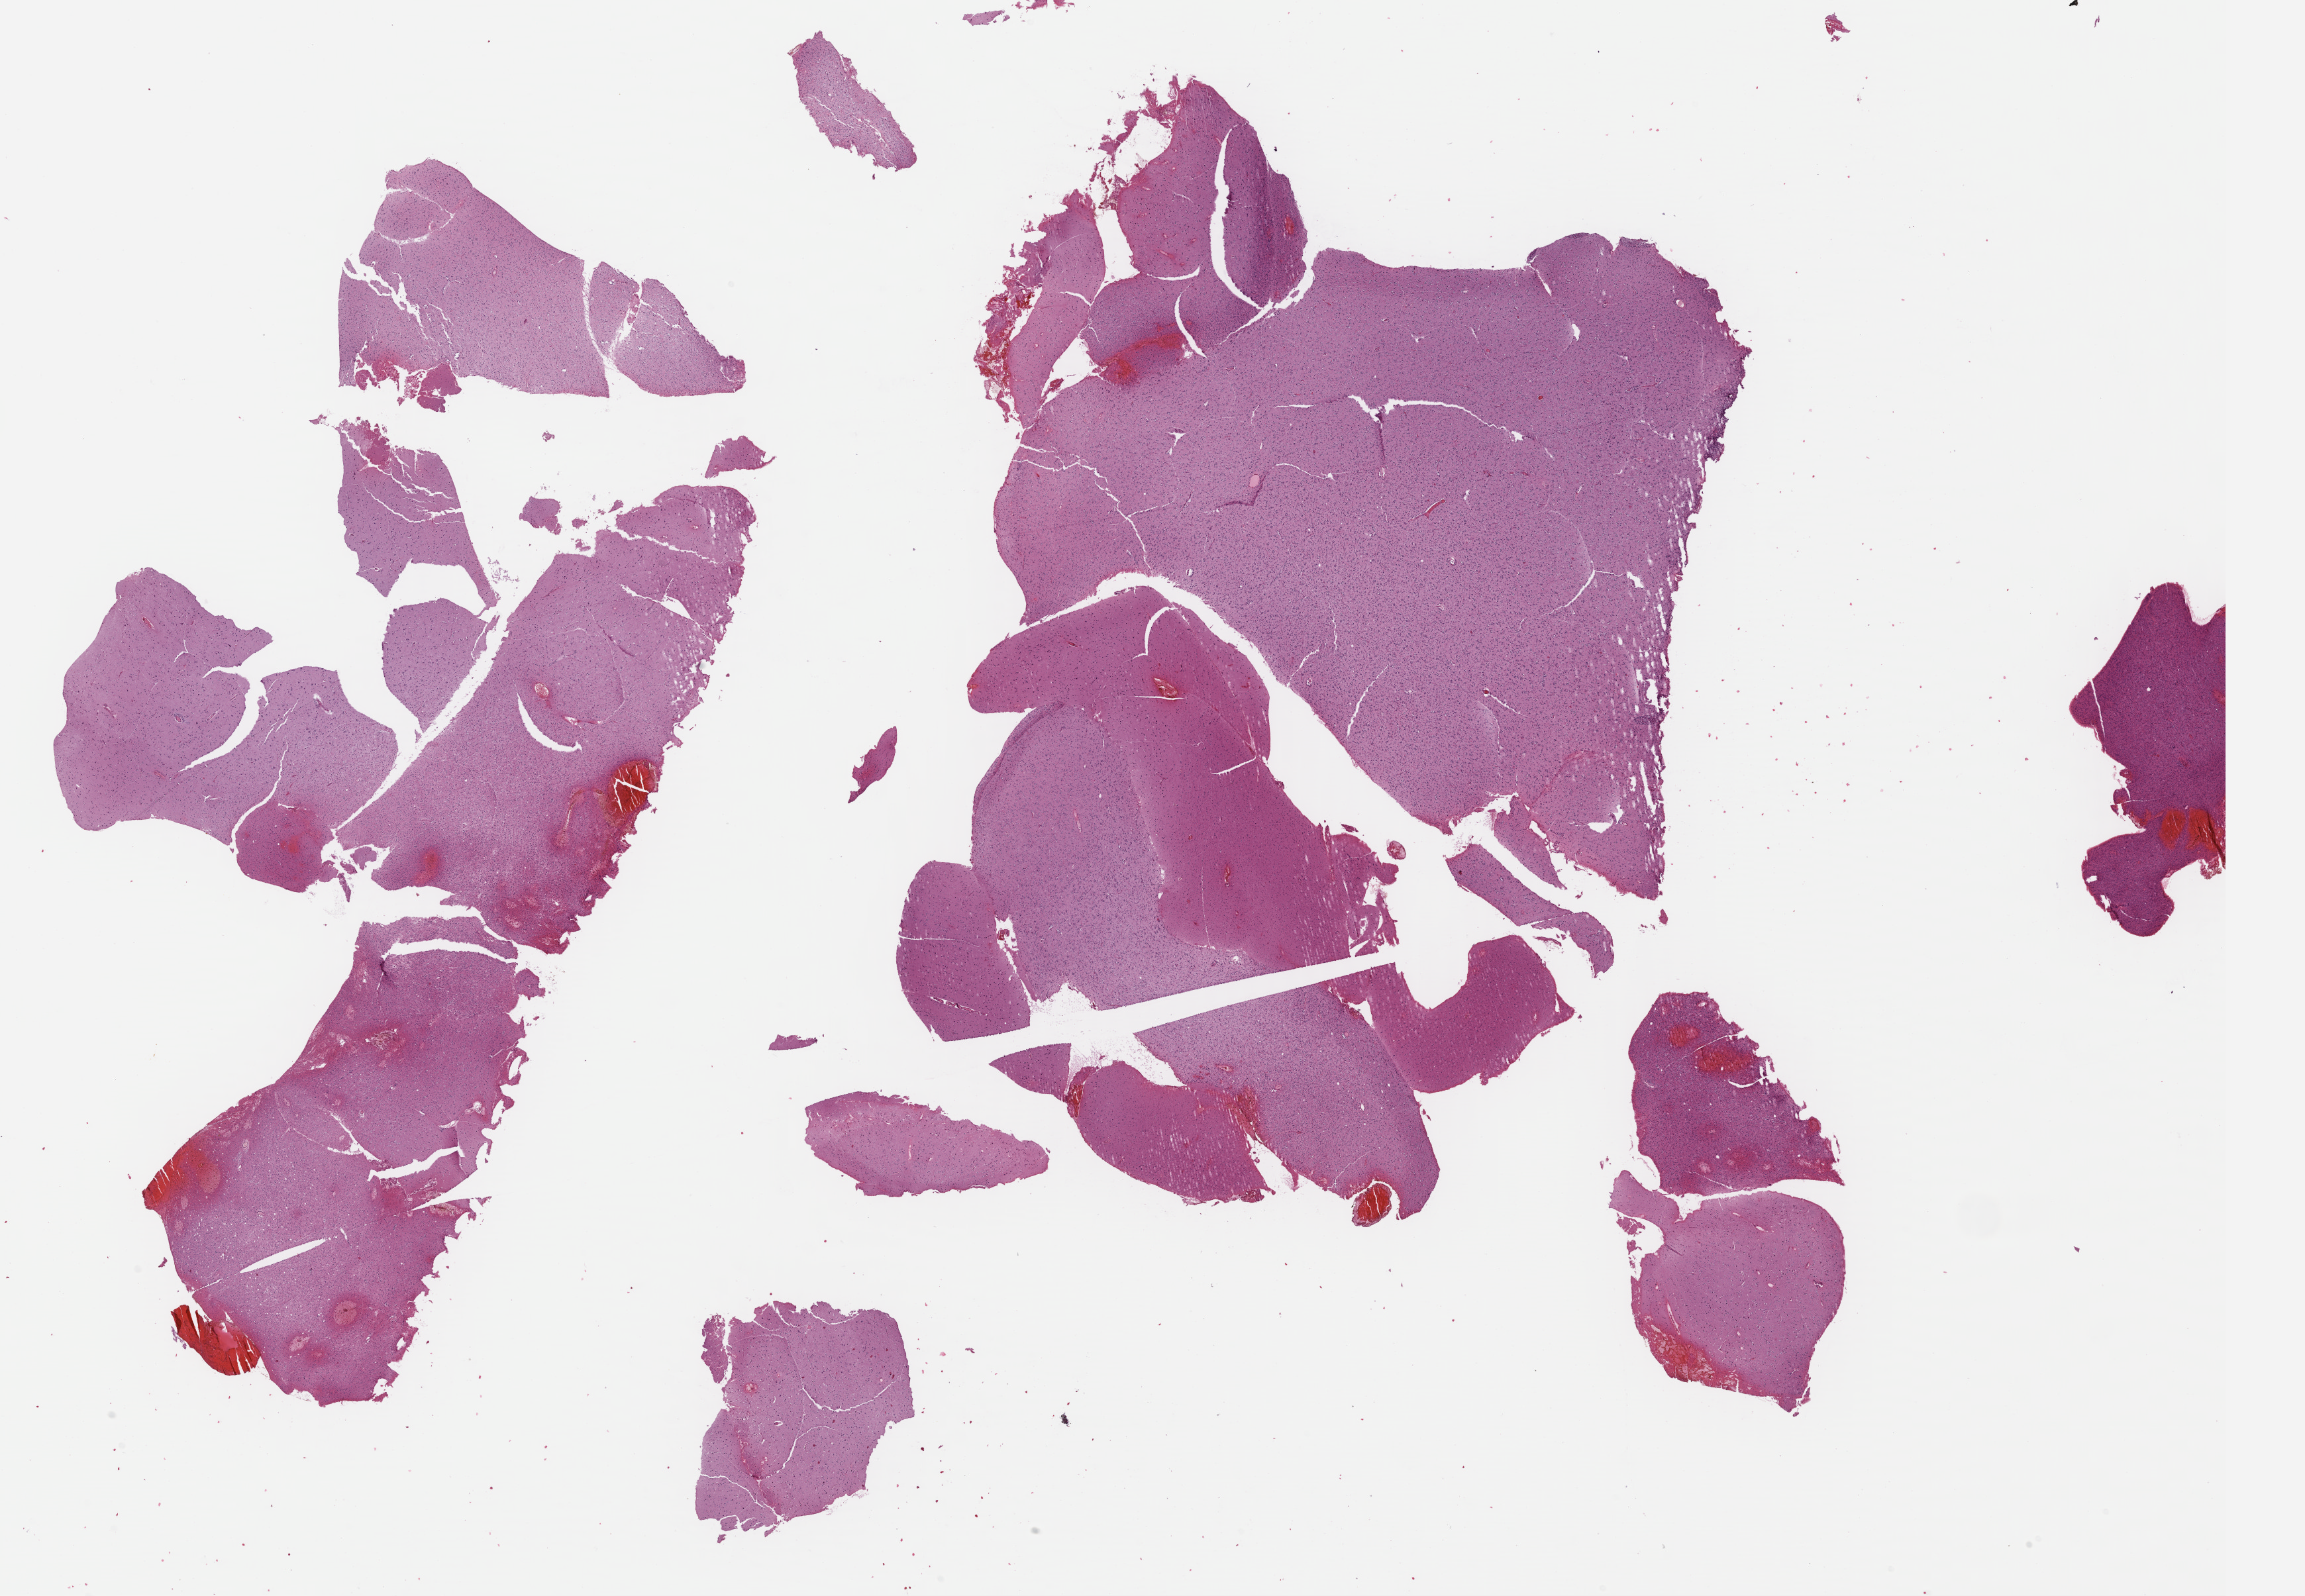
H&E-stained whole-slide image — whole scanned area (about 27.4 x 18.9 mm, acquisition: 40x scan) shown as a low-resolution overview. Formalin-fixed paraffin-embedded (FFPE) diagnostic section. Primary tumour sample from the brain. Patient: female, age at initial diagnosis 20 years. Histologic grade: G2 (moderately differentiated).
Pathologic diagnosis: Oligodendroglioma, NOS.